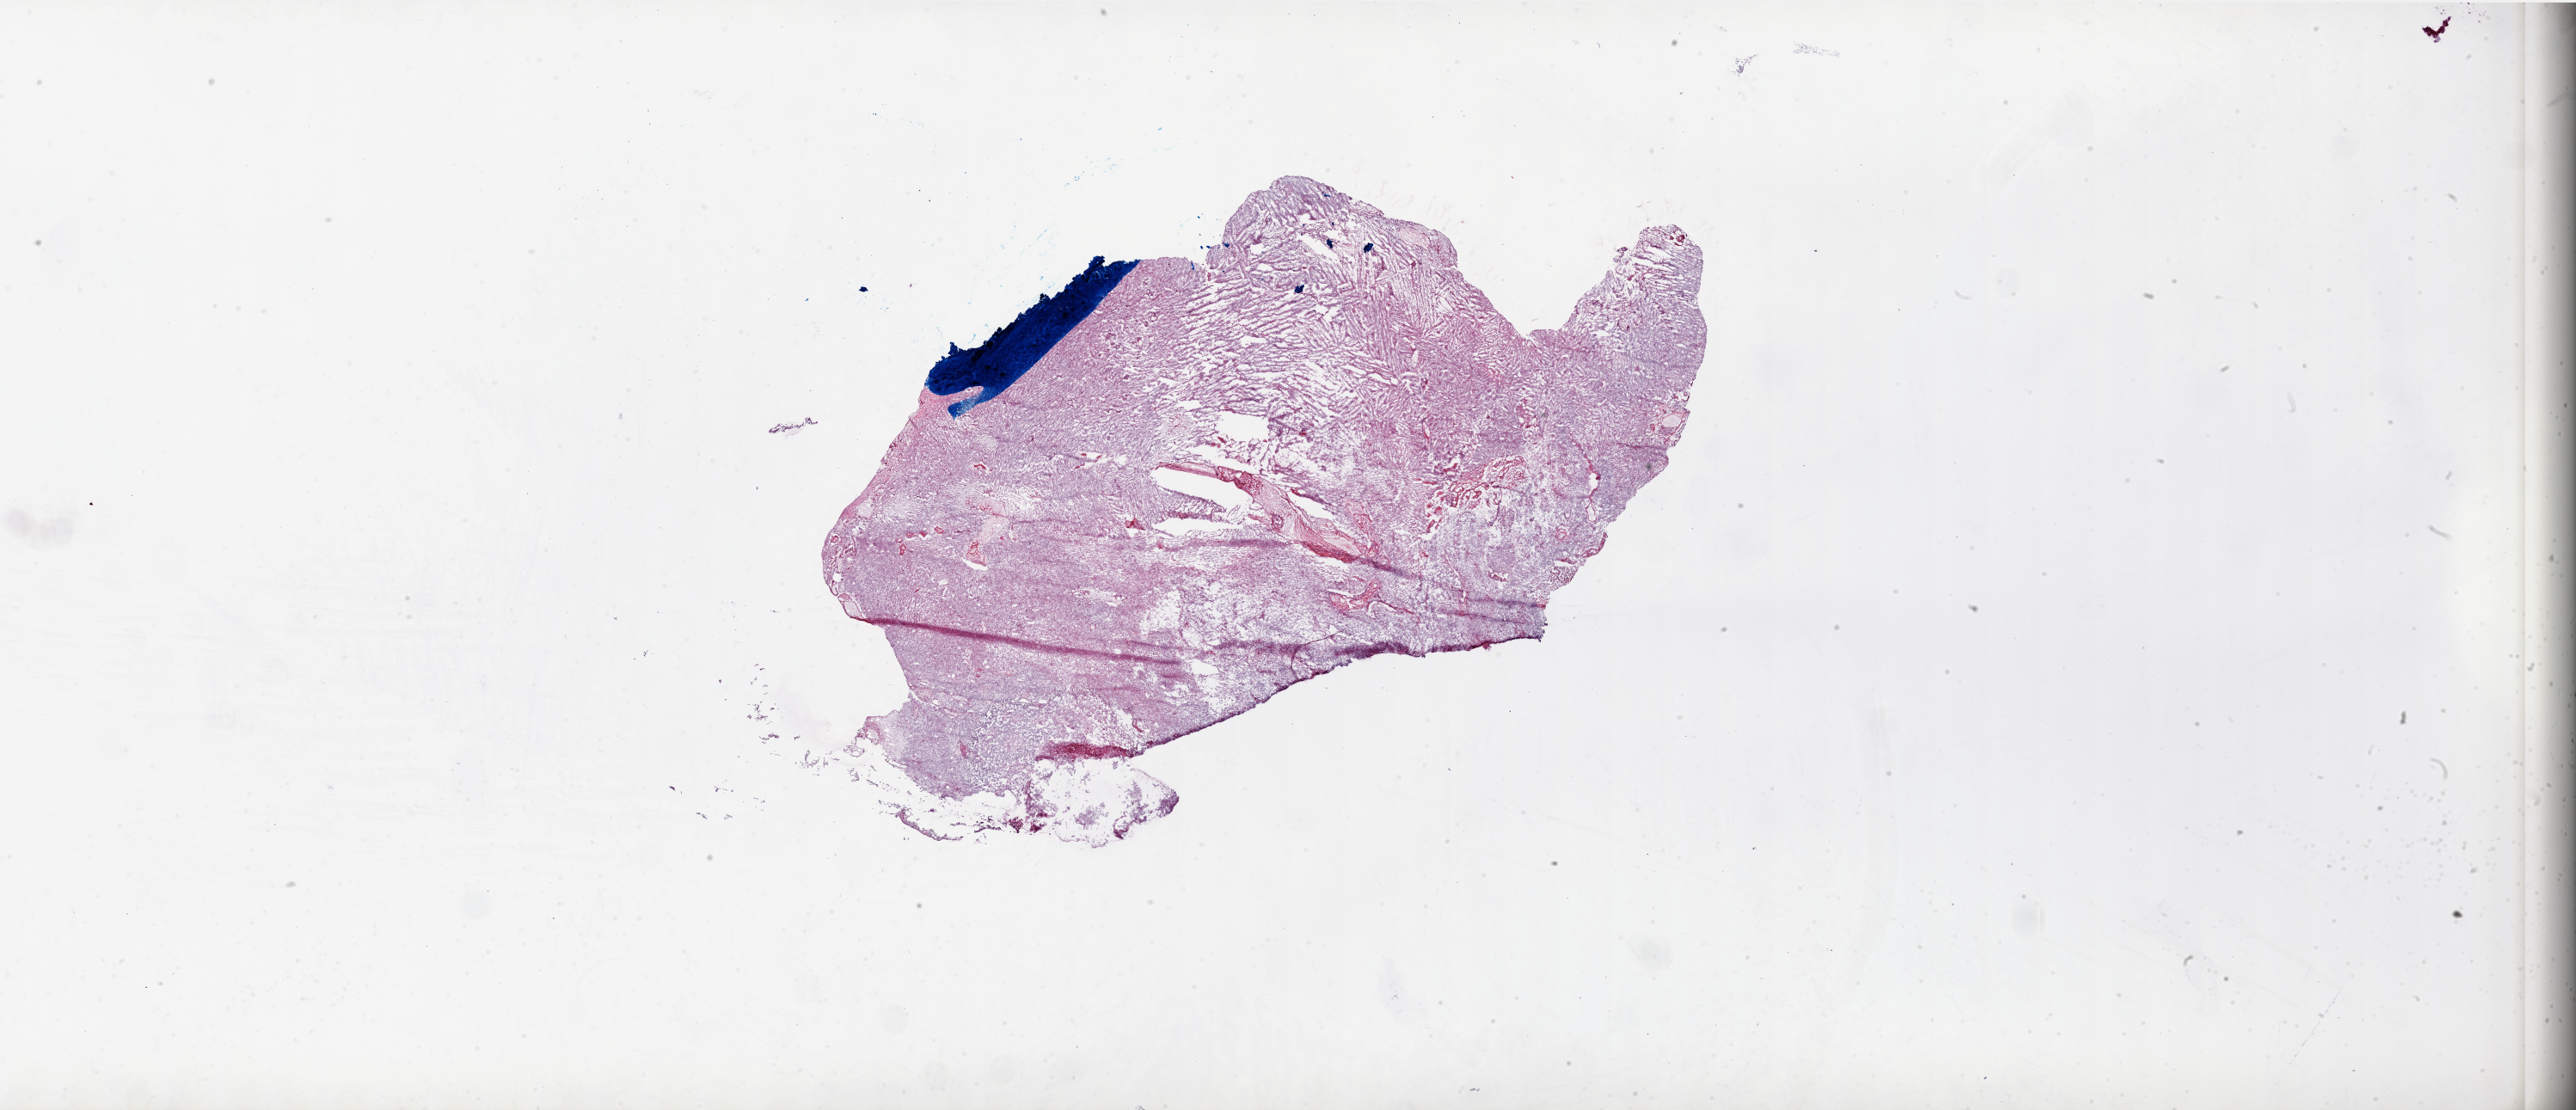
Digitized Hematoxylin and eosin (H&E) stained tissue section (whole slide), a low-resolution overview of the entire scanned area, about 48.0 x 20.7 mm, frozen section from the top of the tissue portion, sample: primary tumour, brain. Male patient; age at initial diagnosis 62 years. Pathologist review of this section (percent, as recorded): tumour cells 90%, tumour nuclei 100%, normal cells 0%, stromal cells 0%, necrosis 10%. Inflammatory infiltration, as recorded: lymphocyte infiltration 0%.
- pathologic diagnosis: Glioblastoma